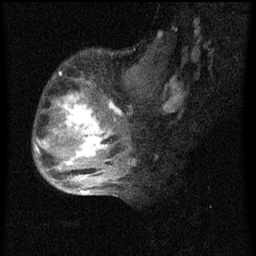
Breast MRI (dynamic contrast-enhanced), one sagittal slice; slice 23 of 60 in the series (ordered by position); dynamic contrast-enhanced series, image 2 of 4 at this slice position (ordered by acquisition); 1.5 T; TE 4.2 ms, TR 8 ms; 2 mm slice thickness; 256 × 256 image matrix, field of view 180 × 180 mm. Female patient, age 50 years.
Outlined on this slice (semi-automatic segmentation, software-assisted and operator-edited):
- analysis volume of interest (the breast-tissue region the enhancement analysis was run in; not a lesion): bounding box (x1, y1, x2, y2) in pixels: (34, 62, 124, 177)
- tumour enhancement mask (voxels above the 70 % enhancement threshold inside the analysis volume of interest): (35, 94, 123, 165)